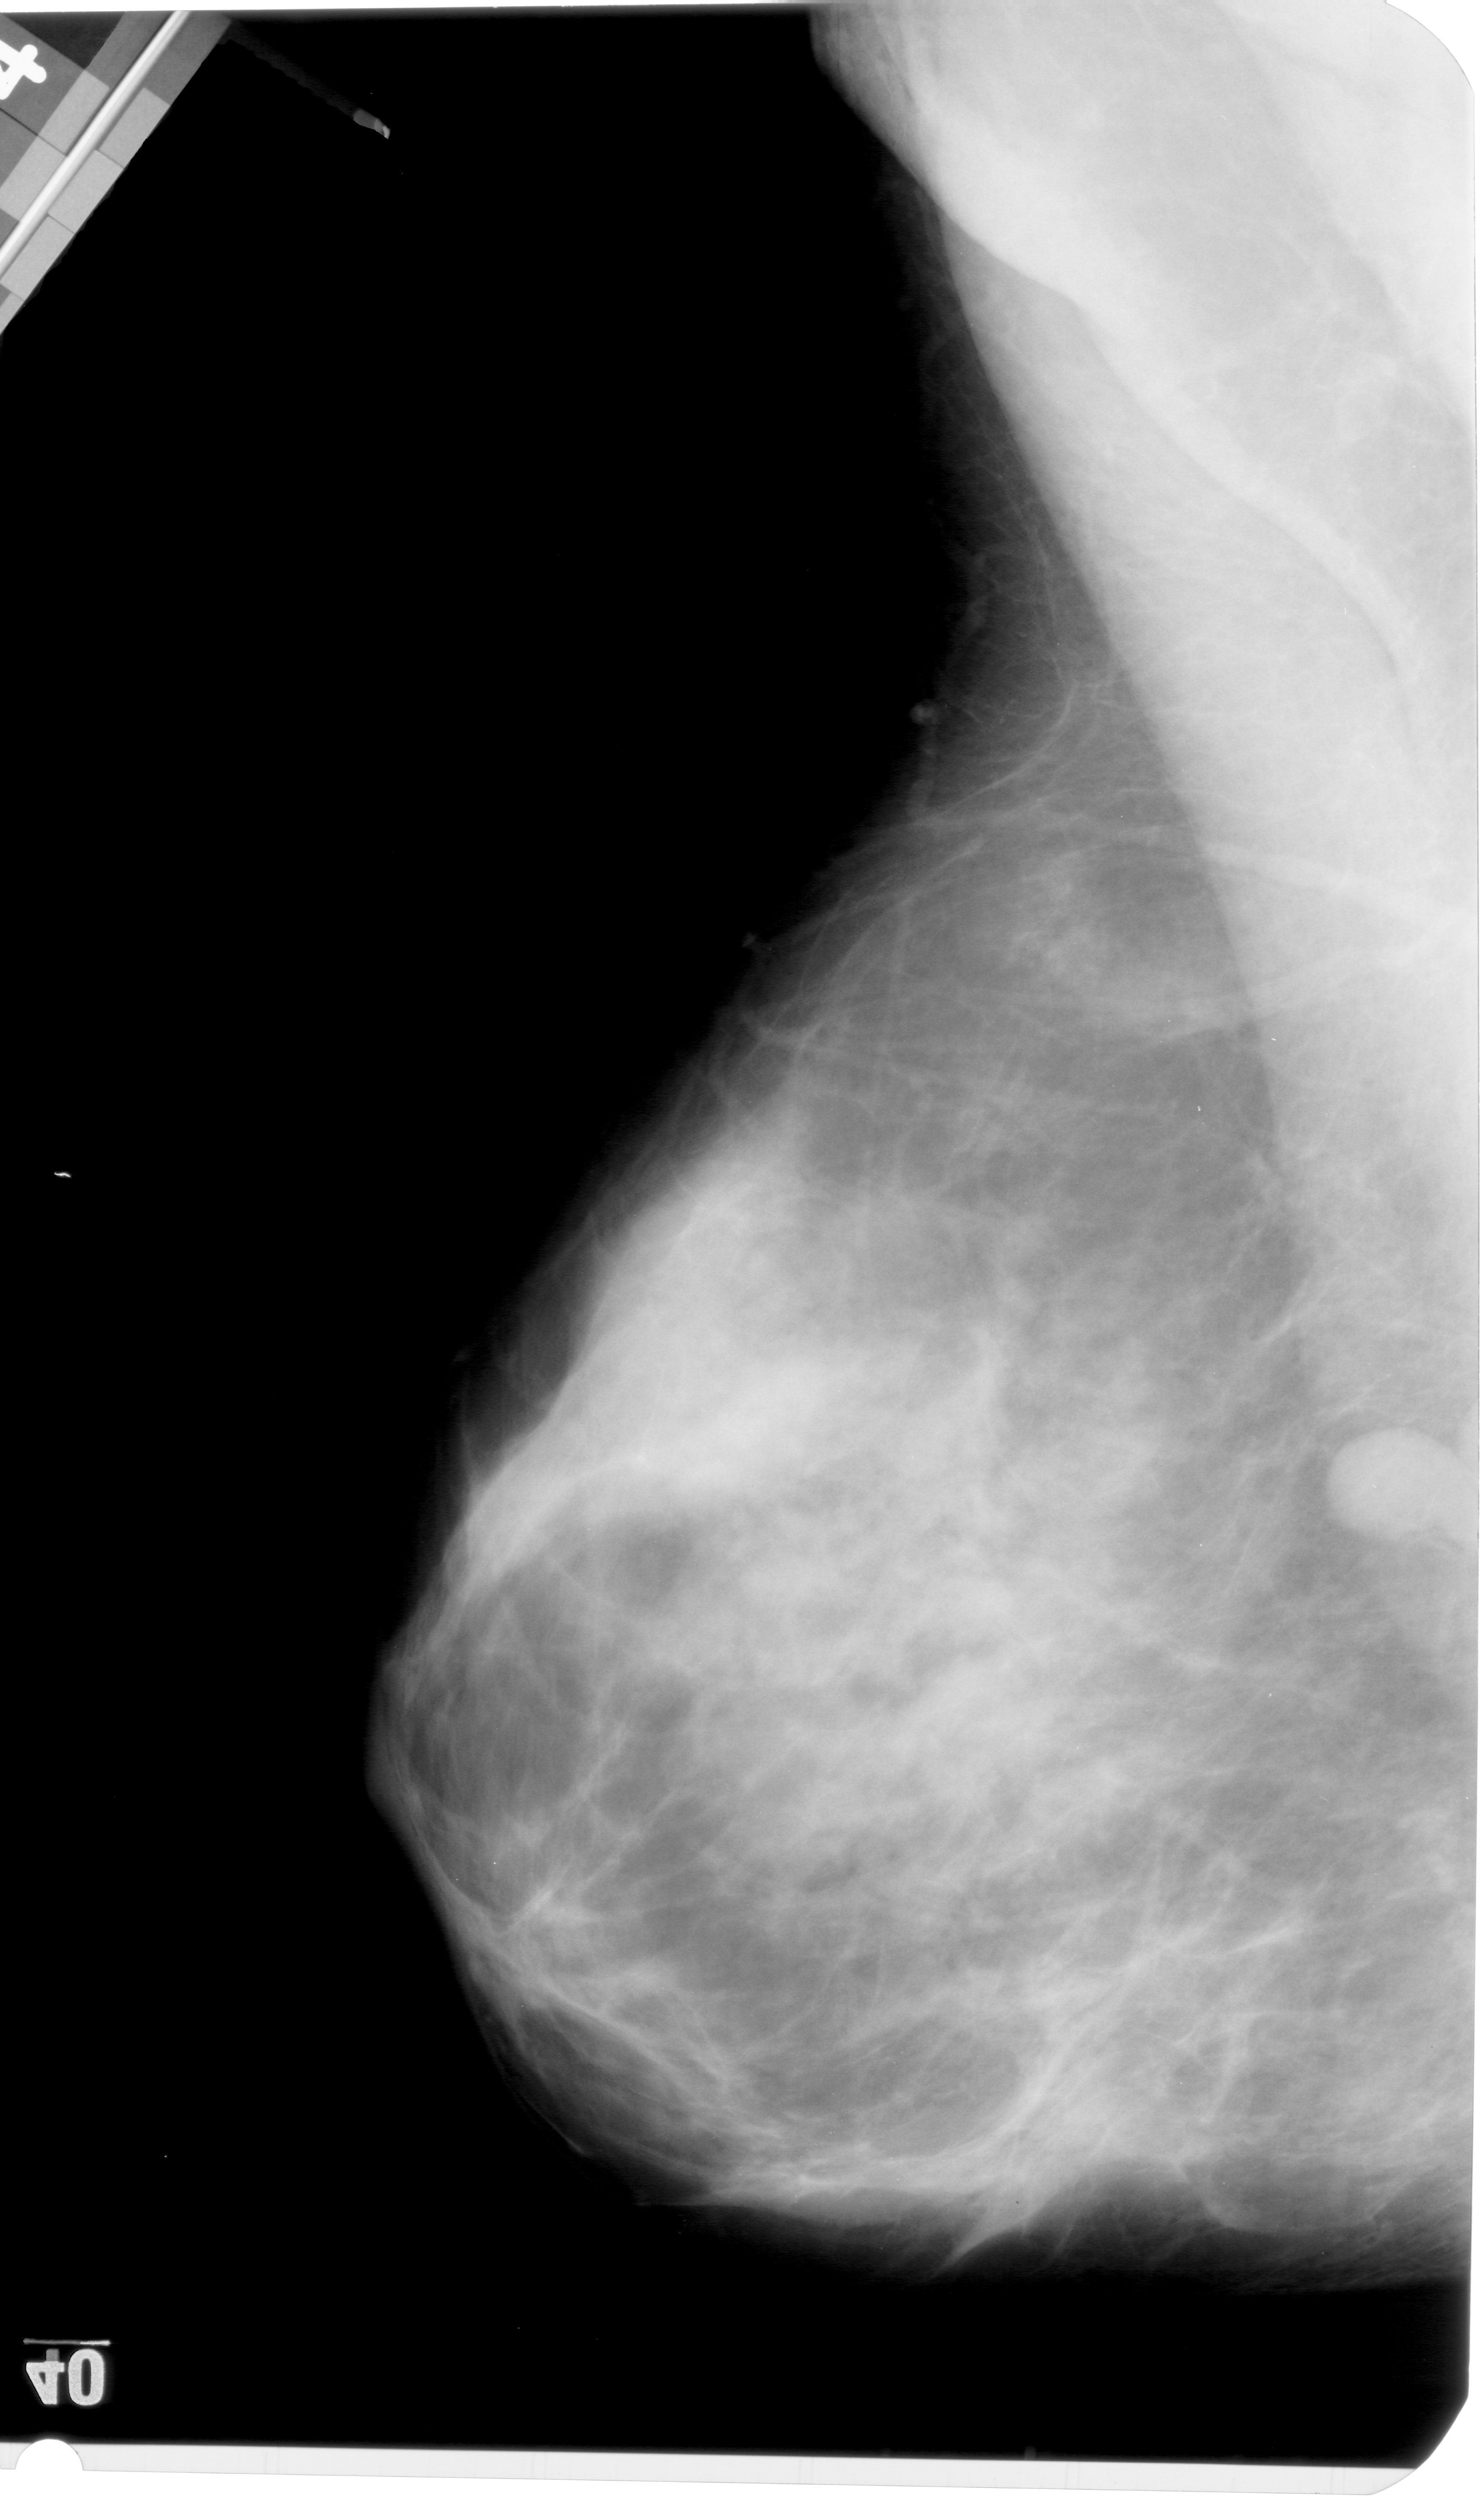
Scanned film-screen mammogram; left breast; MLO view; BI-RADS breast density category 4 (scale 1–4); 1484 × 2515 image matrix.
Expert-marked regions of interest on this film, with their recorded descriptors:
- mass, shape lobulated, margins circumscribed; BI-RADS assessment category 4; pathology result (as recorded, not read from the image): benign: bounding box <1316,1419,1451,1555> (left, top, right, bottom; pixels)